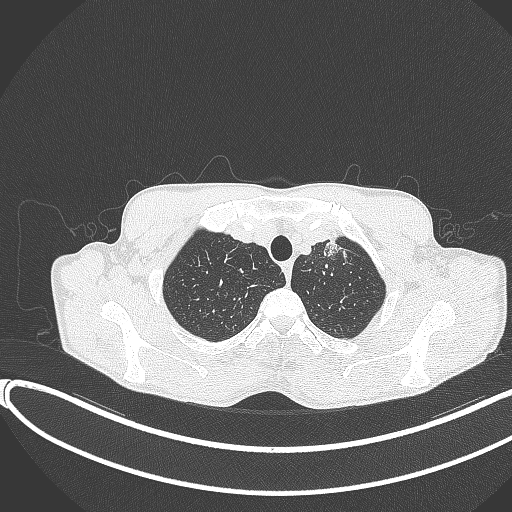
Chest CT, one axial slice. Slice 338 of 374 in the series (ordered by position). 120 kVp. Lung window (W 1500 / L -600 HU). 1 mm slice thickness. 512 × 512 image matrix, field of view 400 × 400 mm. Patient: male, 58 years. Case-level facts recorded for this patient, not image findings: clinical TNM (as recorded): T1c N1 M0.
Outlined on this slice (bounding box drawn by a radiologist):
- lung tumour (recorded histology: adenocarcinoma): bounding box (x1, y1, x2, y2) in pixels: (319, 233, 345, 257)